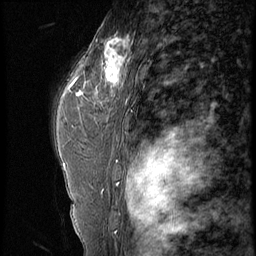
Breast MRI (dynamic contrast-enhanced), one sagittal slice; 4 images stored at this slice position (order not interpretable as contrast timing); 1.5 T; TE 4.2 ms, TR 9 ms; 256 × 256 image matrix. Female patient, age 44 years. From the clinical record (not read from this slice): setting: breast cancer imaged before/during neoadjuvant chemotherapy; receptor status: triple-negative.
Annotated regions visible in this slice (semi-automatically segmented with operator editing):
- analysis volume of interest (the breast-tissue region the enhancement analysis was run in; not a lesion): box from (x=87, y=28) to (x=132, y=99) px
- tumour enhancement mask (voxels above the 140 % enhancement threshold inside the analysis volume of interest): (x=87, y=35)–(x=129, y=89)